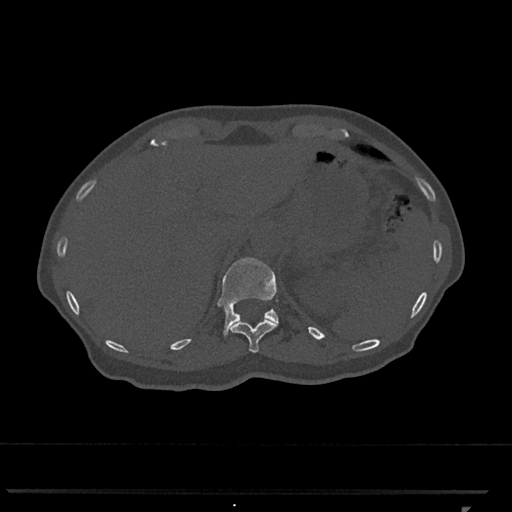
CT including the spine, one axial slice. Position 491 of 793 along the scan axis. Reconstruction kernel Br40s/3. Bone window (W 1800 / L 400 HU). 512 × 512 image matrix, field of view 380 × 380 mm. Female patient, age 62 years. Case-level facts recorded for this patient, not image findings: primary cancer: renal.
Structures marked on this image (semi-automatically segmented with operator editing):
- T11 vertebra: box from (x=230, y=319) to (x=278, y=353) px
- T12 vertebra: (x=217, y=257)–(x=279, y=337)